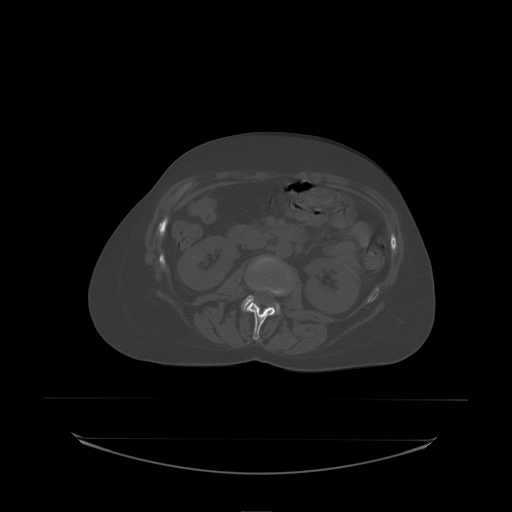
CT including the spine, one axial slice. Slice 68 of 242 in the series (ordered by position). Bone window (W 1800 / L 400 HU). 2.5 mm slice thickness. 512 × 512 image matrix, field of view 500 × 500 mm. Female patient, age 53 years. From the clinical record (not read from this slice): primary cancer: lung.
Annotated regions visible in this slice (semi-automatic segmentation, software-assisted and operator-edited):
- L2 vertebra: bounding box <245,286,286,338> (left, top, right, bottom; pixels)
- L3 vertebra: <242,259,281,315>